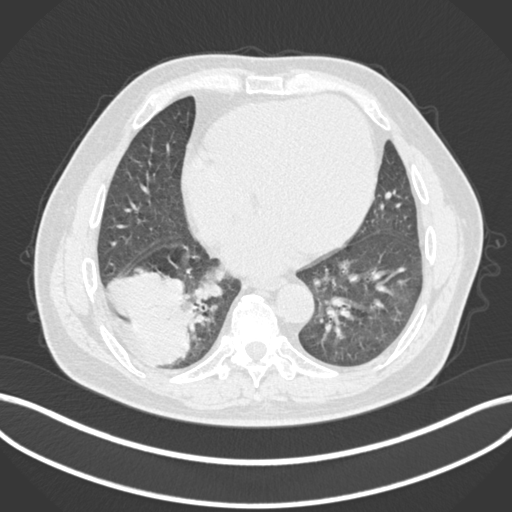
Chest CT, one axial slice; slice 53 of 200 in the series (ordered by position); lung window (W 1500 / L -600 HU); 1 mm slice thickness; 512 × 512 image matrix. Male patient, age 59 years.
Annotated regions visible in this slice (rectangle marked by the reading radiologist):
- lung tumour (recorded histology: adenocarcinoma): bounding box [x1, y1, x2, y2] px = [106, 266, 198, 367]